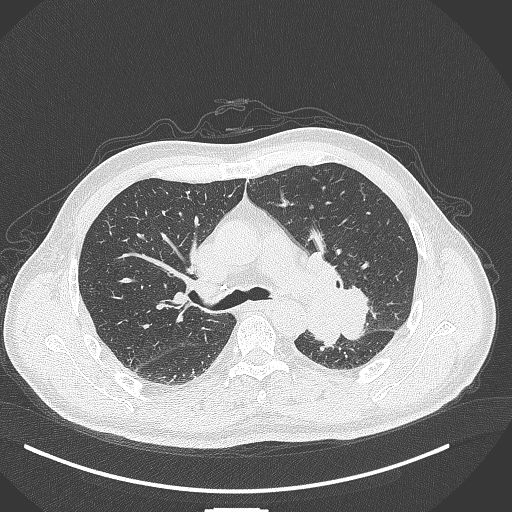
Chest CT, one axial slice. Slice 271 of 429 in the series (ordered by position). 120 kVp. Lung window (W 1500 / L -600 HU). 1 mm slice thickness. 512 × 512 image matrix. Male patient, age 55 years. Case-level facts recorded for this patient, not image findings: clinical TNM (as recorded): T3 N0 M1c.
Outlined on this slice (rectangle marked by the reading radiologist):
- lung tumour (recorded histology: adenocarcinoma): bounding box <309,248,374,343> (left, top, right, bottom; pixels)